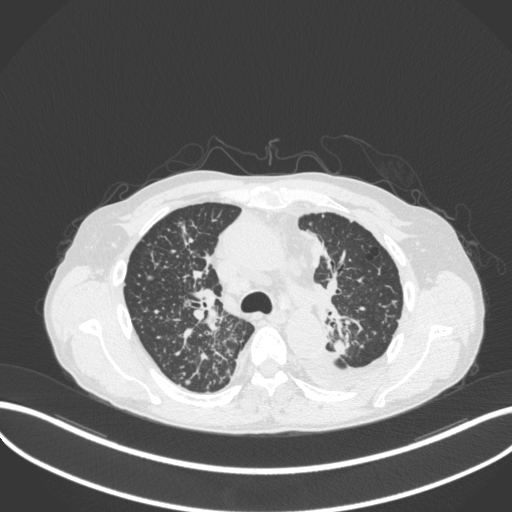
Chest CT, one axial slice. Position 247 of 319 along the scan axis. Lung window (W 1500 / L -600 HU). 1 mm slice thickness. 512 × 512 image matrix, field of view 400 × 400 mm. Male patient, age 58 years. From the clinical record (not read from this slice): clinical TNM (as recorded): T1c N3 M1.
Structures marked on this image (rectangle marked by the reading radiologist):
- lung tumour (recorded histology: adenocarcinoma): bounding box <331,339,357,361> (left, top, right, bottom; pixels)